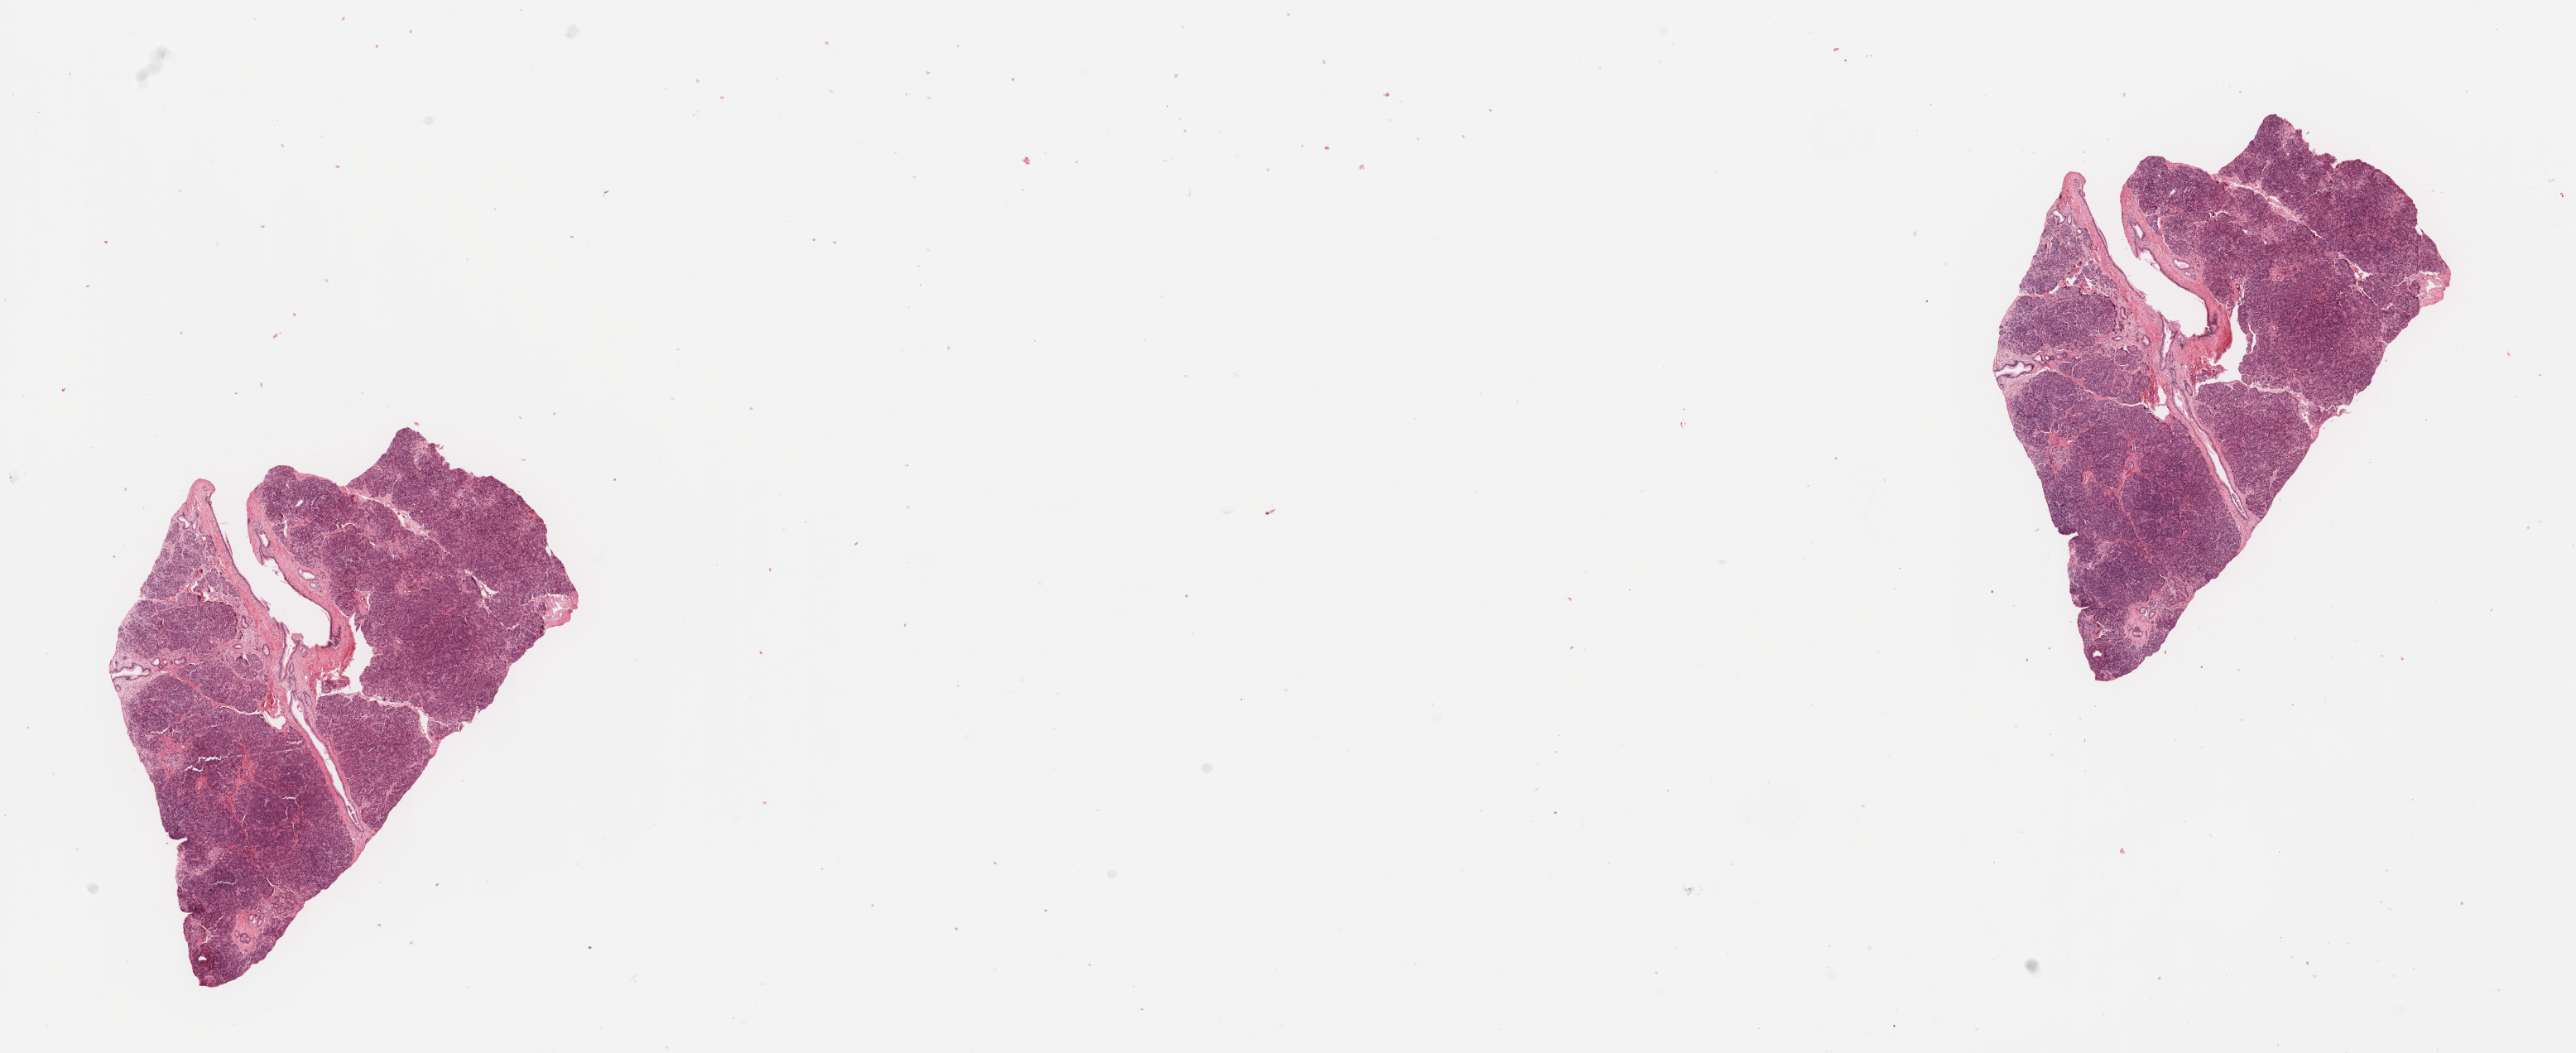
Digitized H&E tissue section (whole slide), low-resolution overview of the scanned area, about 24.6 x 10.1 mm (acquisition: 20x scan); pancreas, normal (non-tumour) tissue. 71-year-old male patient.
- this section: normal (non-tumour) tissue from the same patient
- patient diagnosis: Infiltrating duct carcinoma, NOS